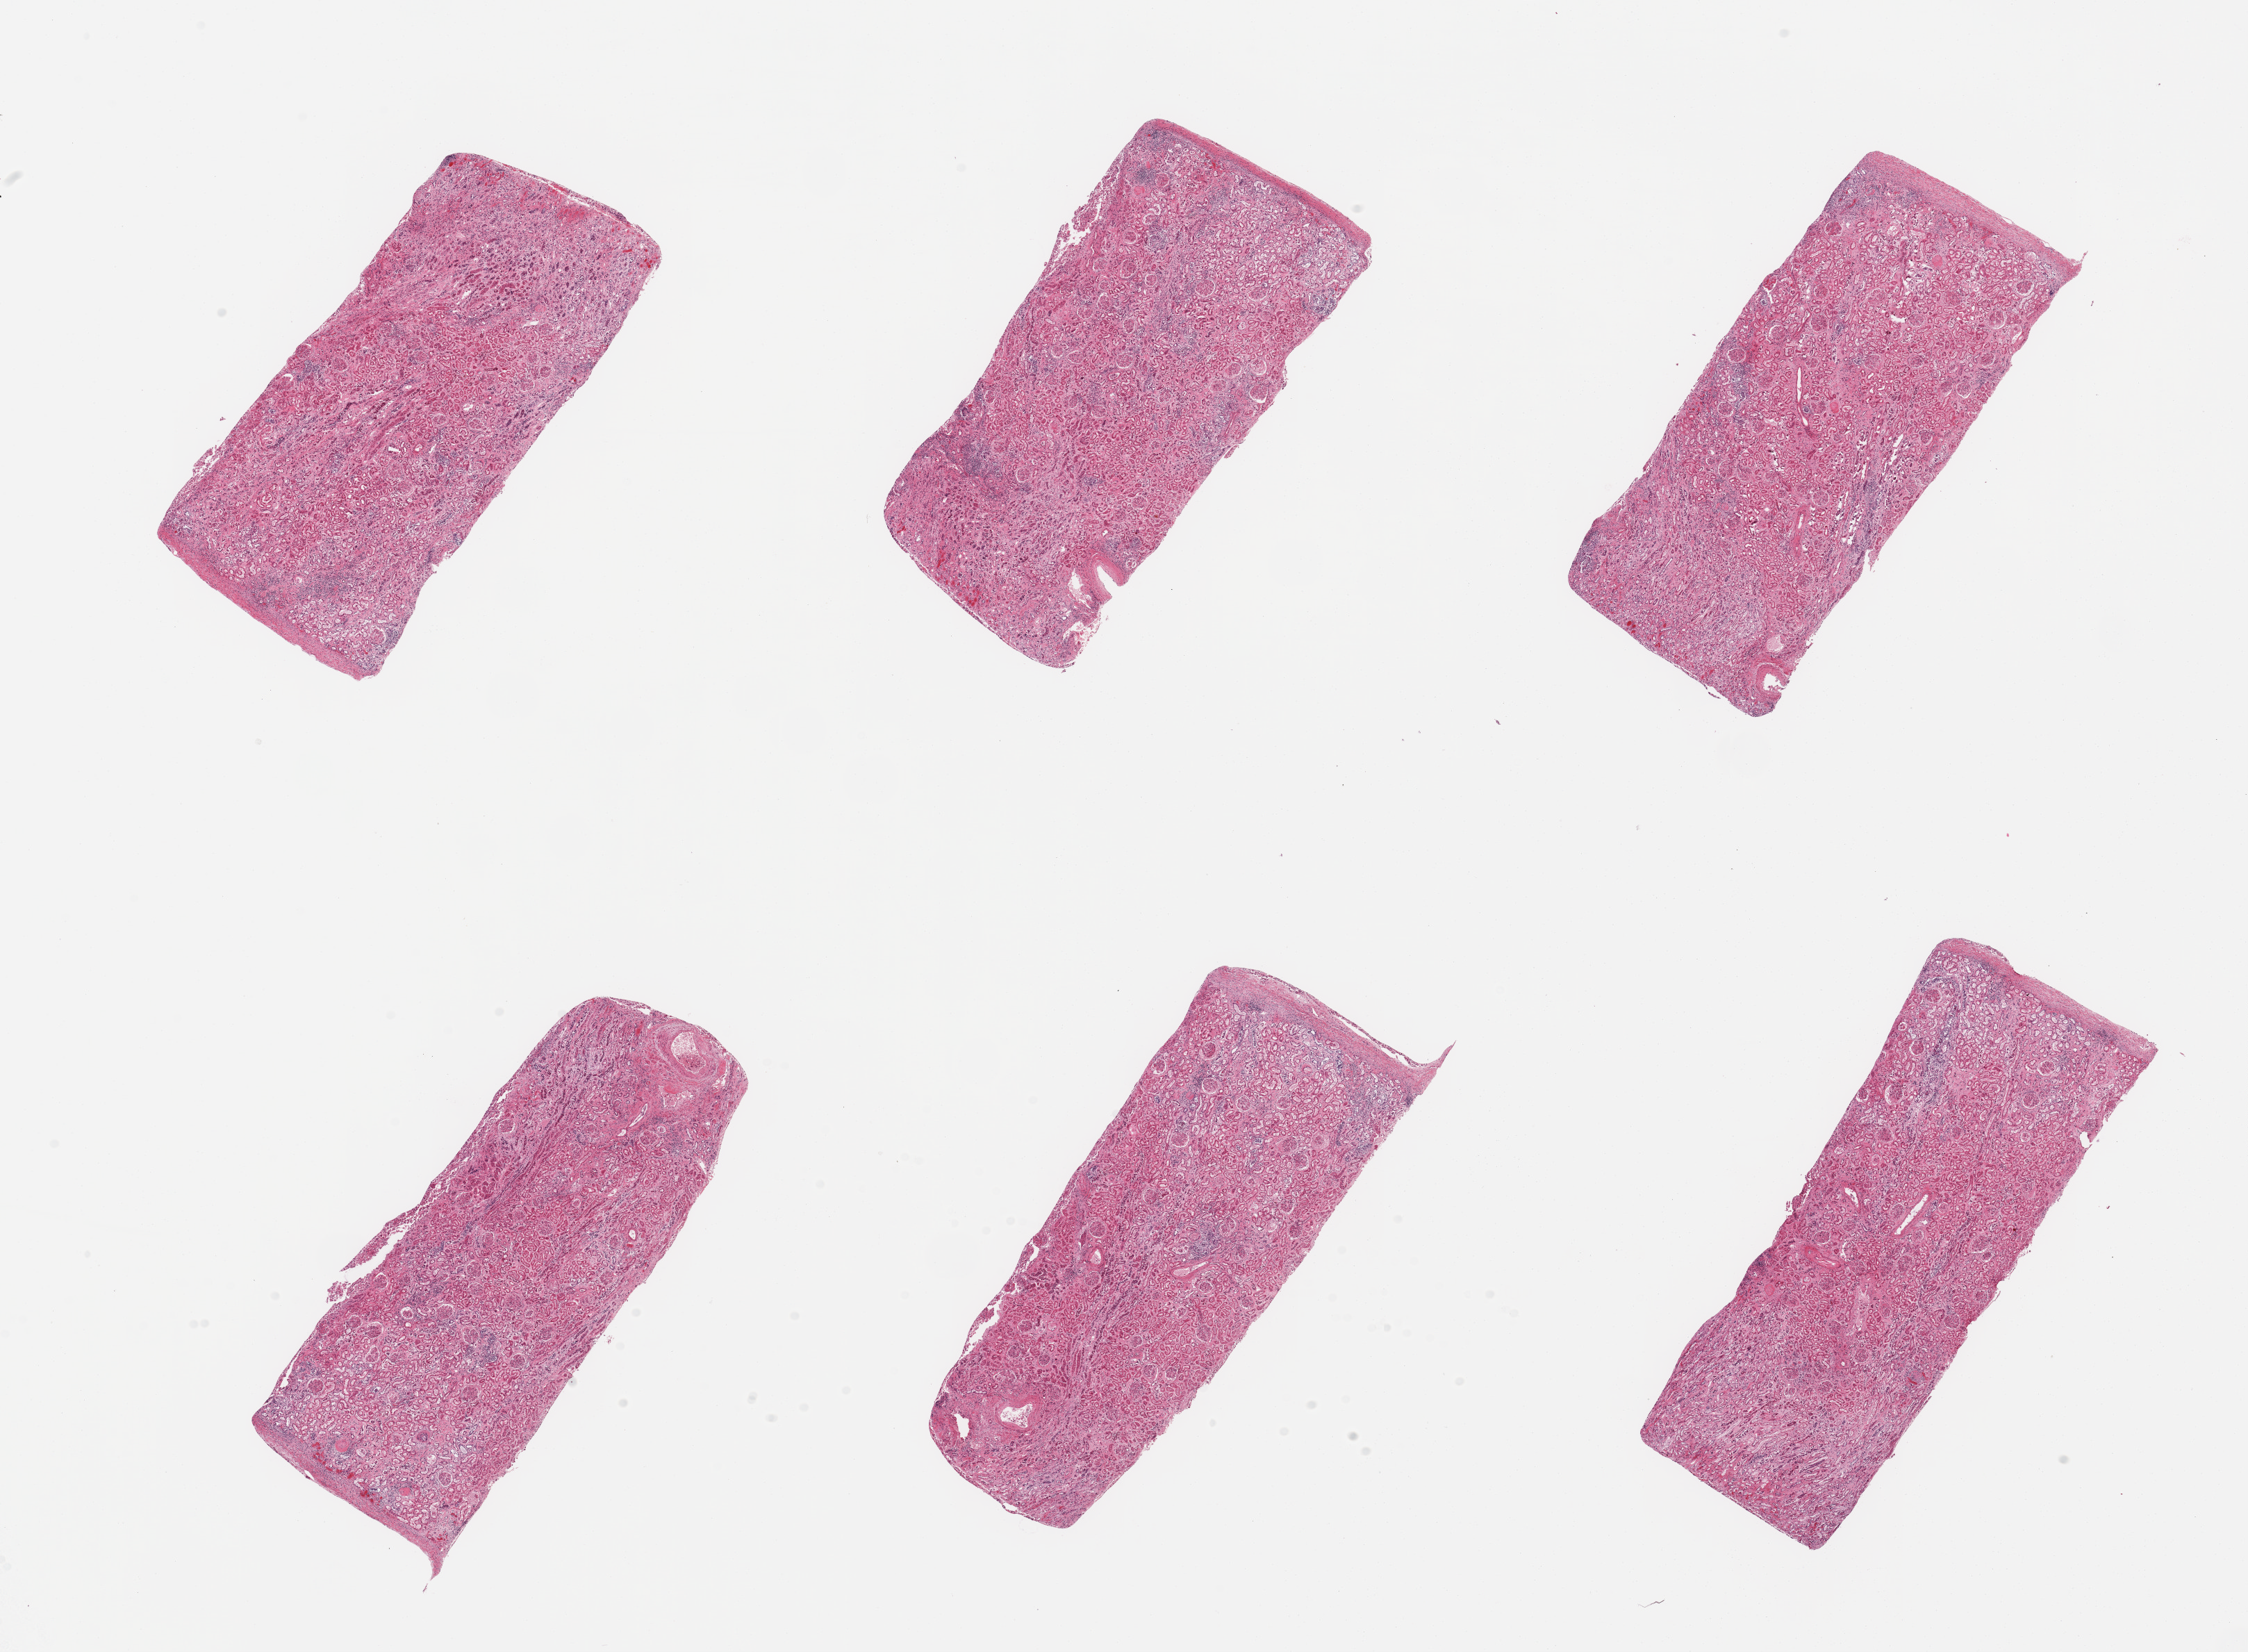
Whole-slide image, H&E stain, brightfield — a low-resolution overview of the entire scanned area, about 25.6 x 18.8 mm, PAXgene-fixed paraffin-embedded (PFPE) section, target tissue: renal cortex, tissue donor sample. Donor sex: male.
Reviewer comment on this tissue sample: 6 pieces, glomeruli present; moderate tubular autolysis.